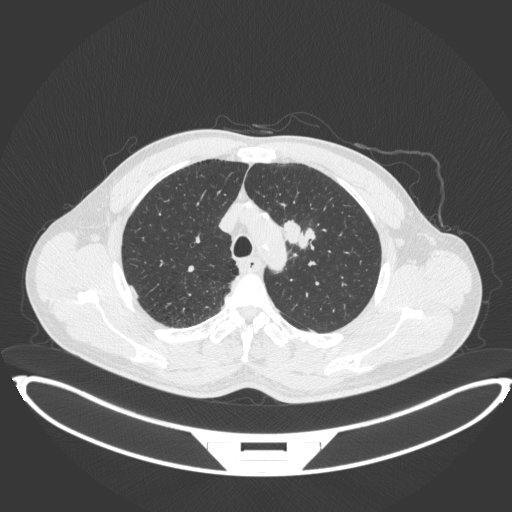
Chest CT, one axial slice. Position 335 of 407 along the scan axis. Reconstruction kernel B31f. 120 kVp. Lung window (W 1500 / L -600 HU). 1 mm slice thickness. 512 × 512 image matrix, field of view 457 × 457 mm. Male patient, age 60 years. Case-level facts recorded for this patient, not image findings: clinical TNM (as recorded): T2a N0 M0.
Outlined on this slice (bounding box drawn by a radiologist):
- lung tumour (recorded histology: squamous cell carcinoma): bounding box (x1, y1, x2, y2) in pixels: (282, 216, 318, 253)